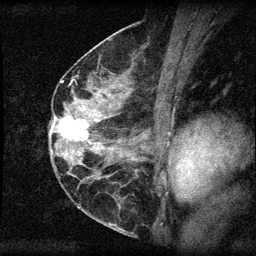
Breast MRI (dynamic contrast-enhanced), one sagittal slice; dynamic contrast-enhanced series, image 2 of 3 at this slice position (ordered by acquisition); 1.5 T; TE 4.2 ms, TR 8.2 ms; 256 × 256 image matrix. Female patient, age 45 years.
Outlined on this slice (semi-automatic segmentation, software-assisted and operator-edited):
- analysis volume of interest (the breast-tissue region the enhancement analysis was run in; not a lesion): box from (x=55, y=110) to (x=94, y=148) px
- tumour enhancement mask (voxels above the 70 % enhancement threshold inside the analysis volume of interest): (x=55, y=117)–(x=88, y=141)